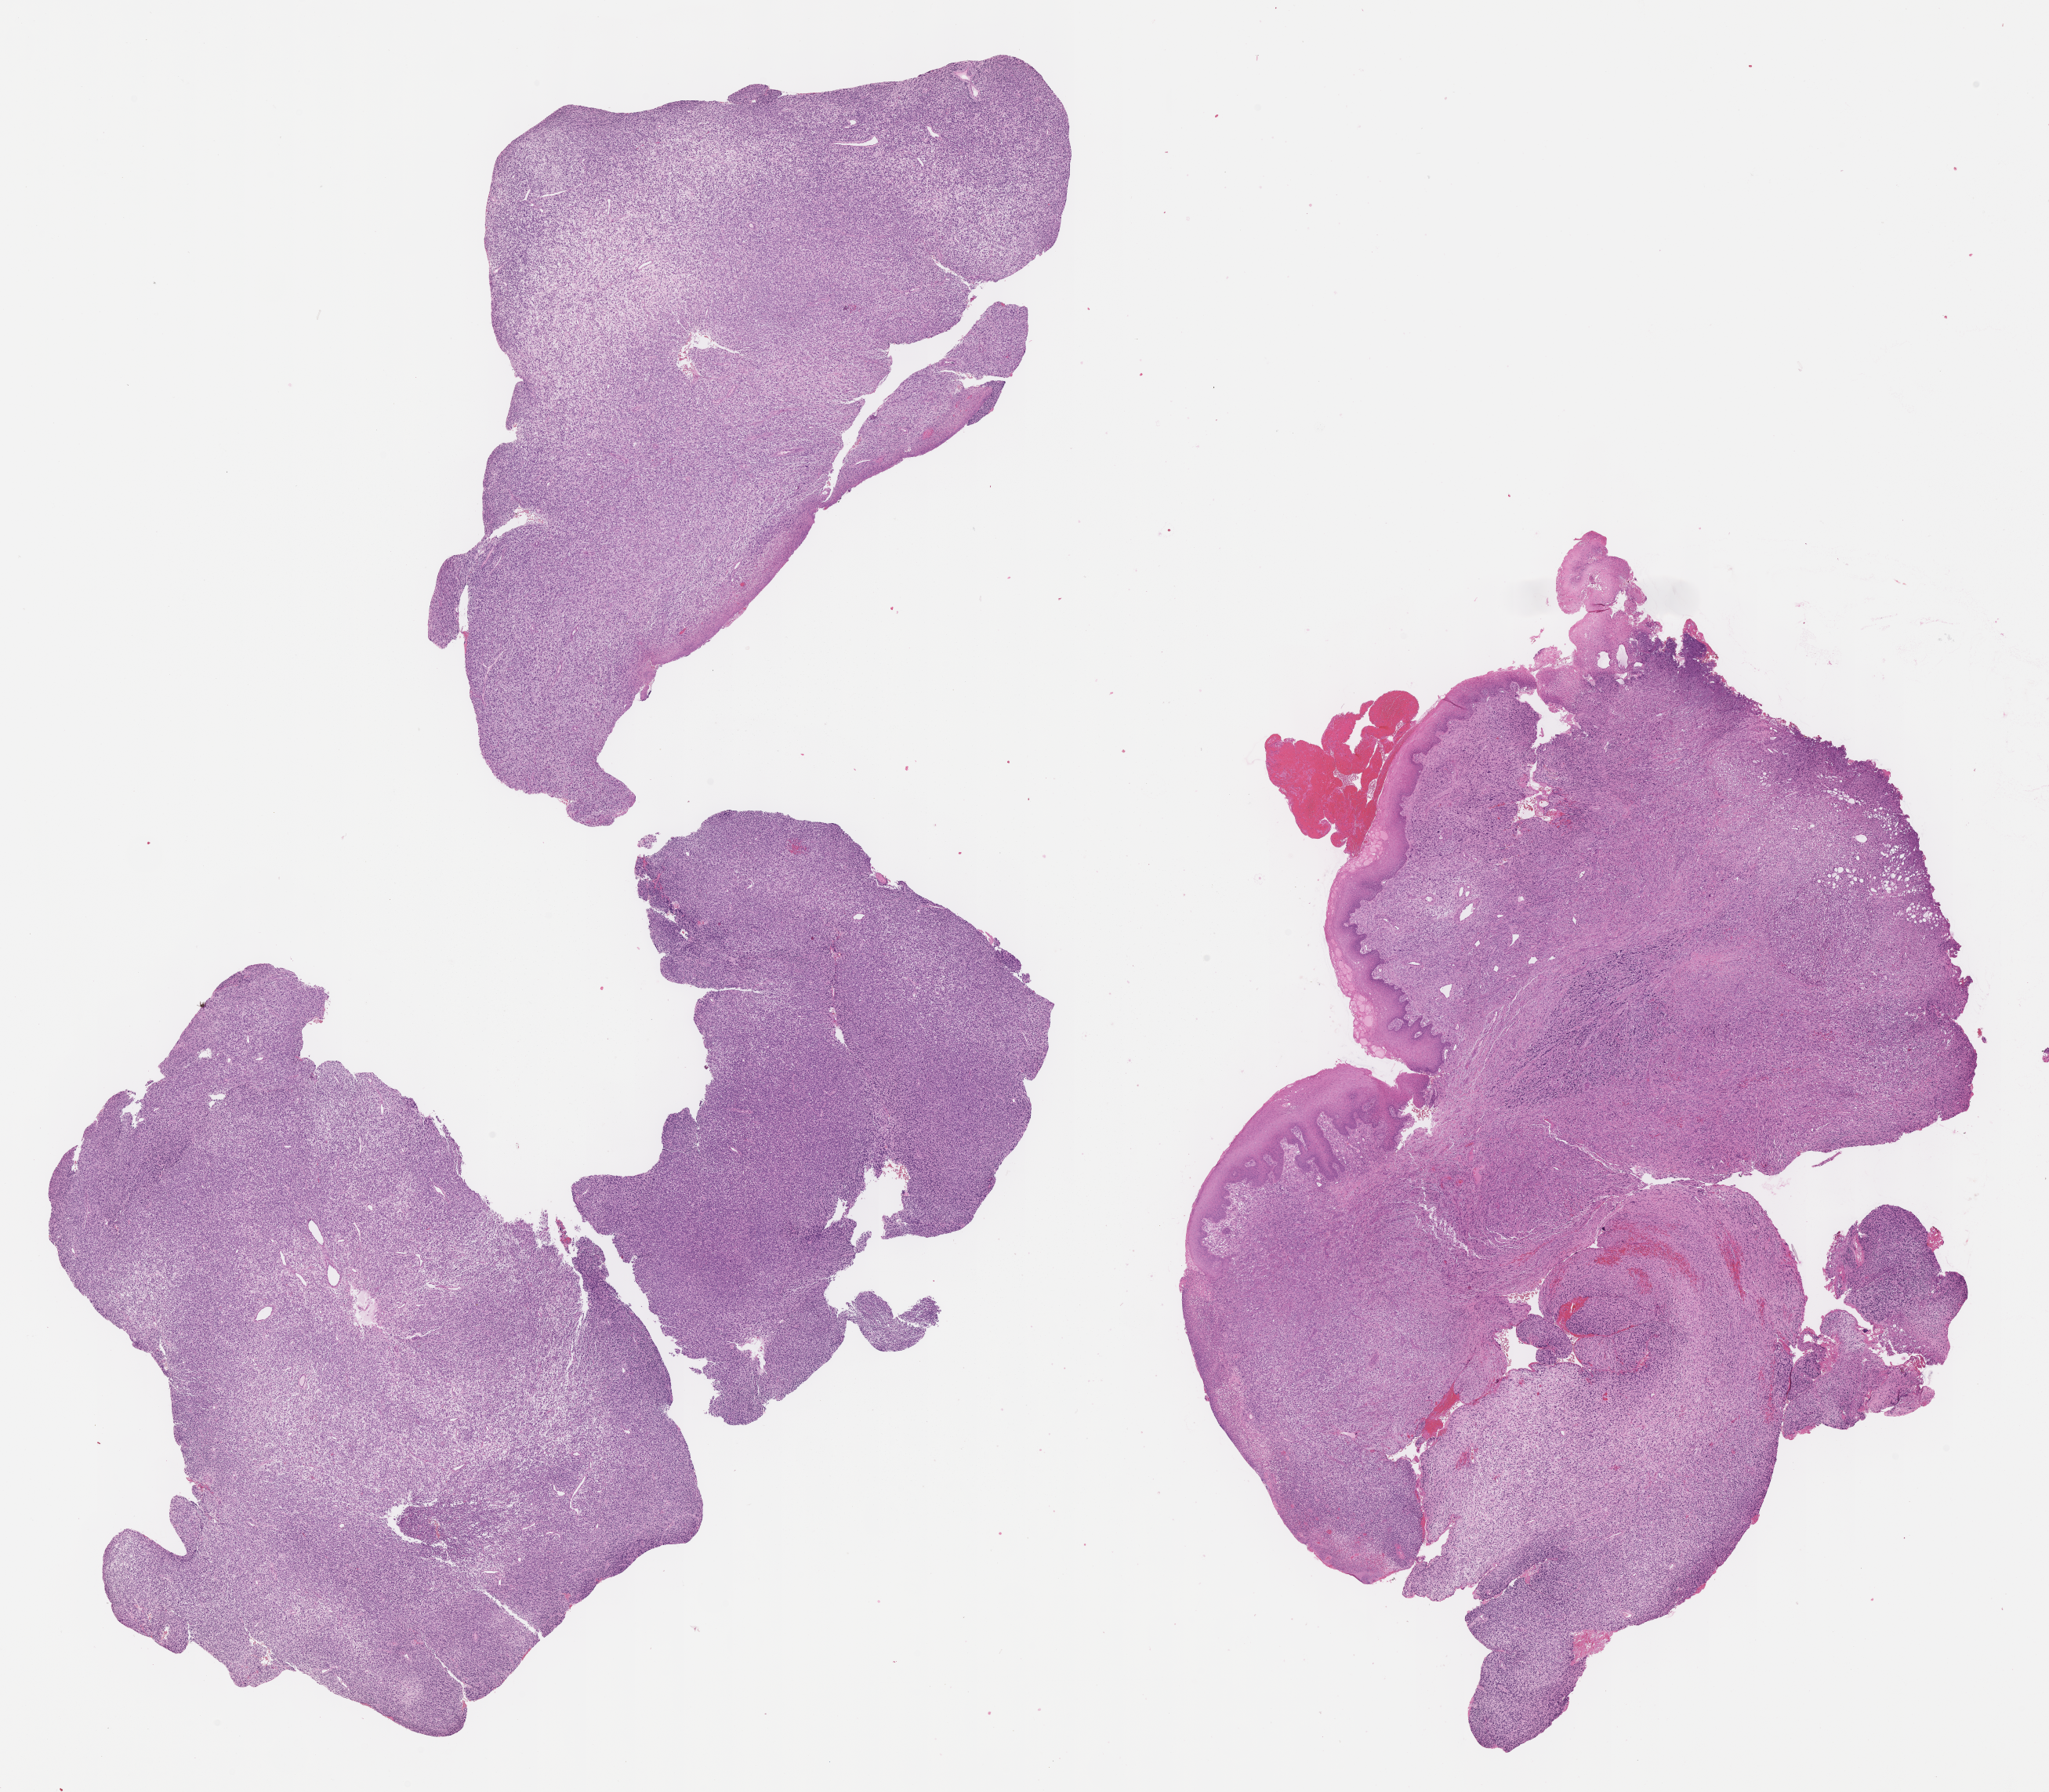
Whole-slide image, H&E stain of tumor tissue, whole scanned area (about 21.1 x 18.5 mm) shown as a low-resolution overview; formalin-fixed, paraffin-embedded (FFPE) tissue; site: cheek, right. Patient: male, age 2.0 years at diagnosis.
Diagnosis: rhabdomyosarcoma; histological classification: embryonal rhabdomyosarcoma. Stage (as recorded): 1. Metastatic status at presentation (as recorded): non-metastatic (confirmed).